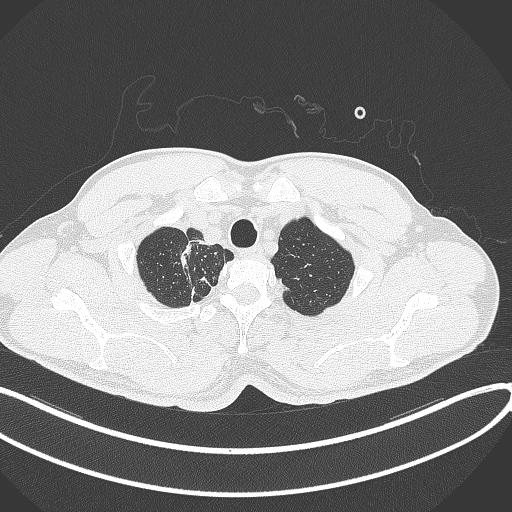
Chest CT, one axial slice; position 339 of 391 along the scan axis; reconstruction kernel B70f; 120 kVp; lung window (W 1500 / L -600 HU); 512 × 512 image matrix, field of view 400 × 400 mm. Patient: male, 48 years. Case-level facts recorded for this patient, not image findings: clinical TNM (as recorded): T1c N1 M1.
Structures marked on this image (rectangle marked by the reading radiologist):
- lung tumour (recorded histology: adenocarcinoma): bounding box <180,241,198,259> (left, top, right, bottom; pixels)